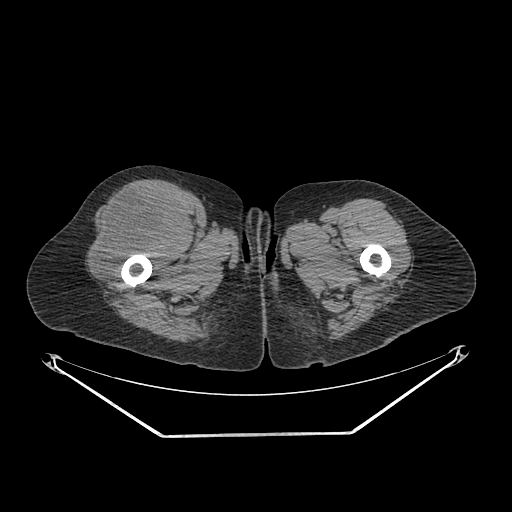
CT of an extremity soft-tissue mass (from a PET/CT study), one axial slice; slice 268 of 311 in the series (ordered by position); reconstruction kernel SOFT; 140 kVp; soft-tissue window (W 400 / L 40 HU); 512 × 512 image matrix. Female patient. From the clinical record (not read from this slice): histological type: pleiomorphic undifferentiated sarcoma; grade: high; site of the primary tumour: right quadricep.
Outlined on this slice (expert contour drawn on MRI and transferred to this co-registered scan by the dataset authors):
- tumour plus oedema (research contour): bounding box [x1, y1, x2, y2] px = [94, 190, 184, 277]
- tumour (research contour): [94, 190, 184, 277]